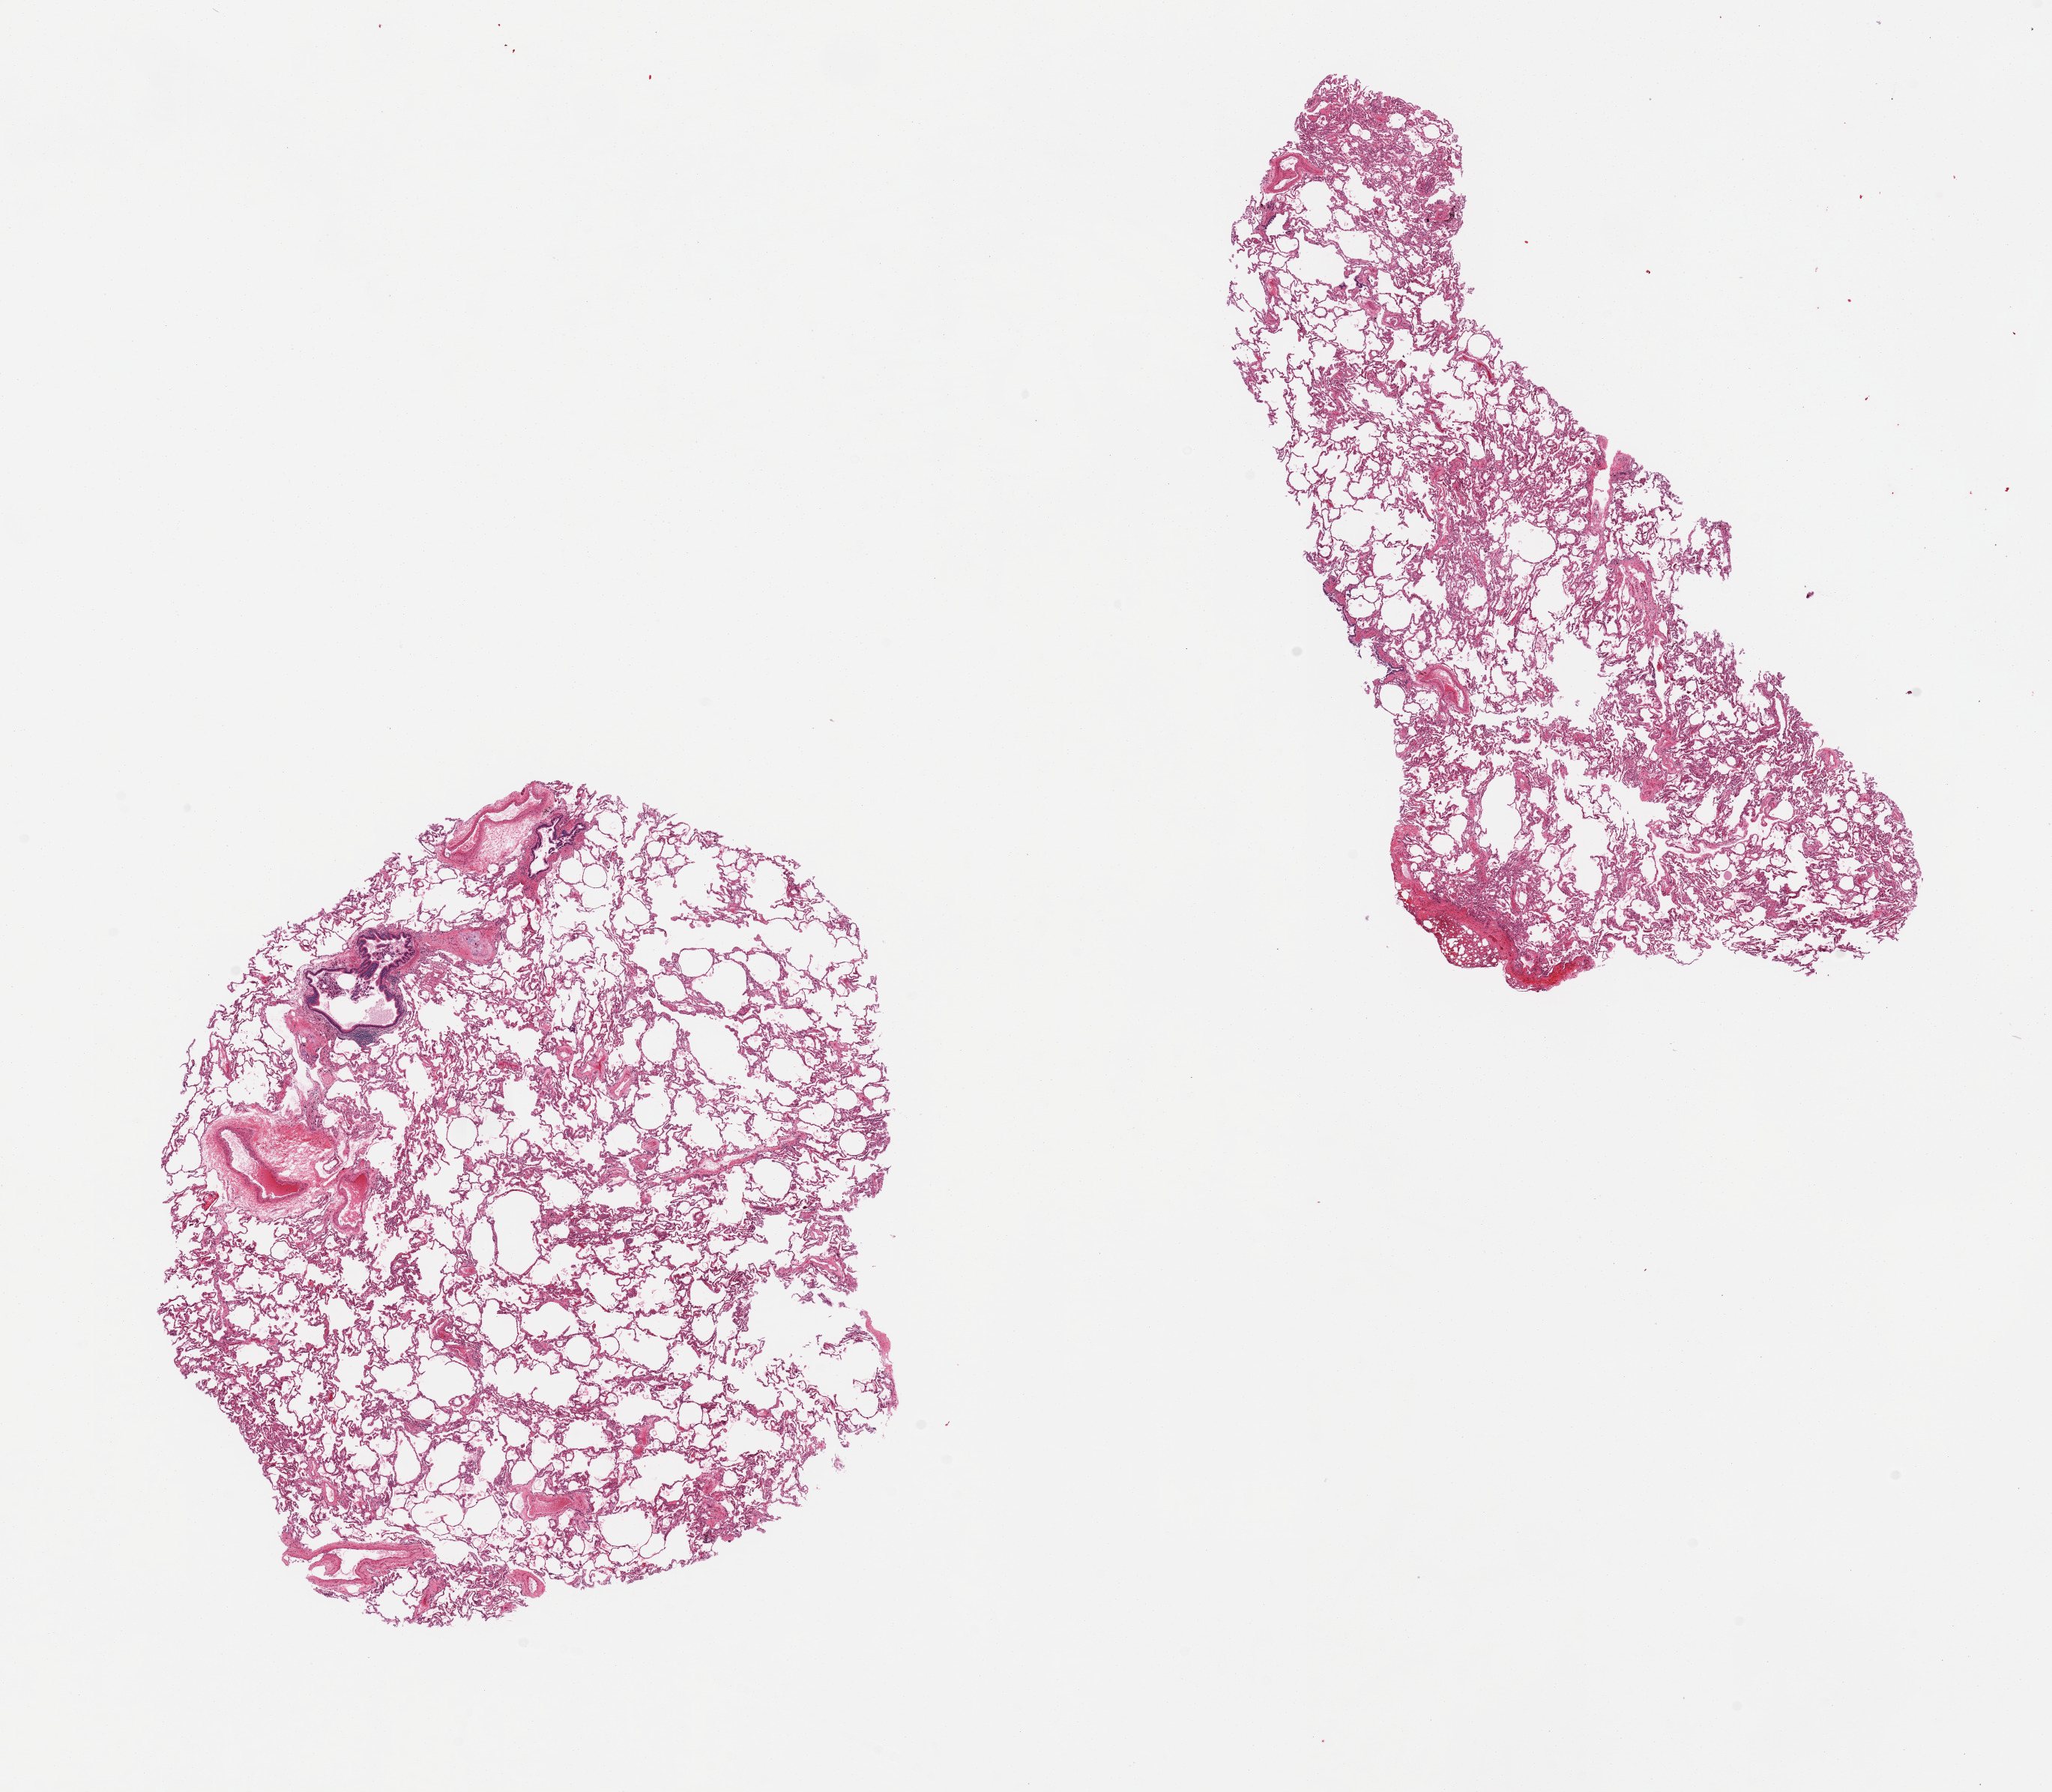
H&E whole-slide image, brightfield, a low-resolution overview of the entire scanned area, about 21.7 x 18.9 mm (acquisition: 20x scan), PAXgene-fixed, paraffin-embedded tissue, sampled site (target tissue): lung, tissue donor sample.
- reviewer comment on this tissue sample: 2 pieces, mild peribronchial inflammation (chronic)